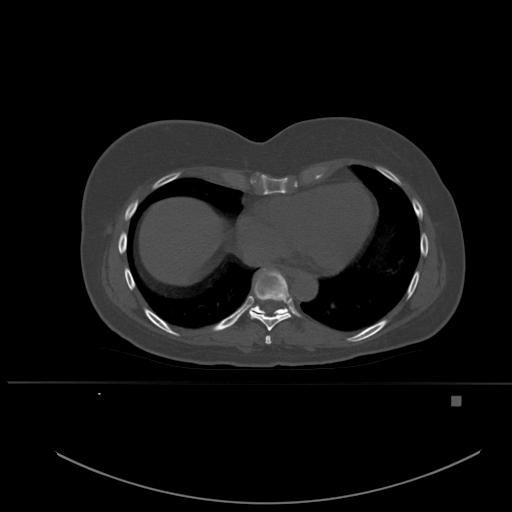
CT including the spine, one axial slice. Position 316 of 651 along the scan axis. Bone window (W 1800 / L 400 HU). 1.5 mm slice thickness. 512 × 512 image matrix, field of view 443 × 443 mm. Female patient, age 49 years. From the clinical record (not read from this slice): primary cancer: breast.
Outlined on this slice (semi-automatically segmented with operator editing):
- T7 vertebra: bounding box [x1, y1, x2, y2] px = [265, 335, 272, 344]
- T8 vertebra: [249, 269, 292, 331]
- T9 vertebra: [228, 270, 288, 320]